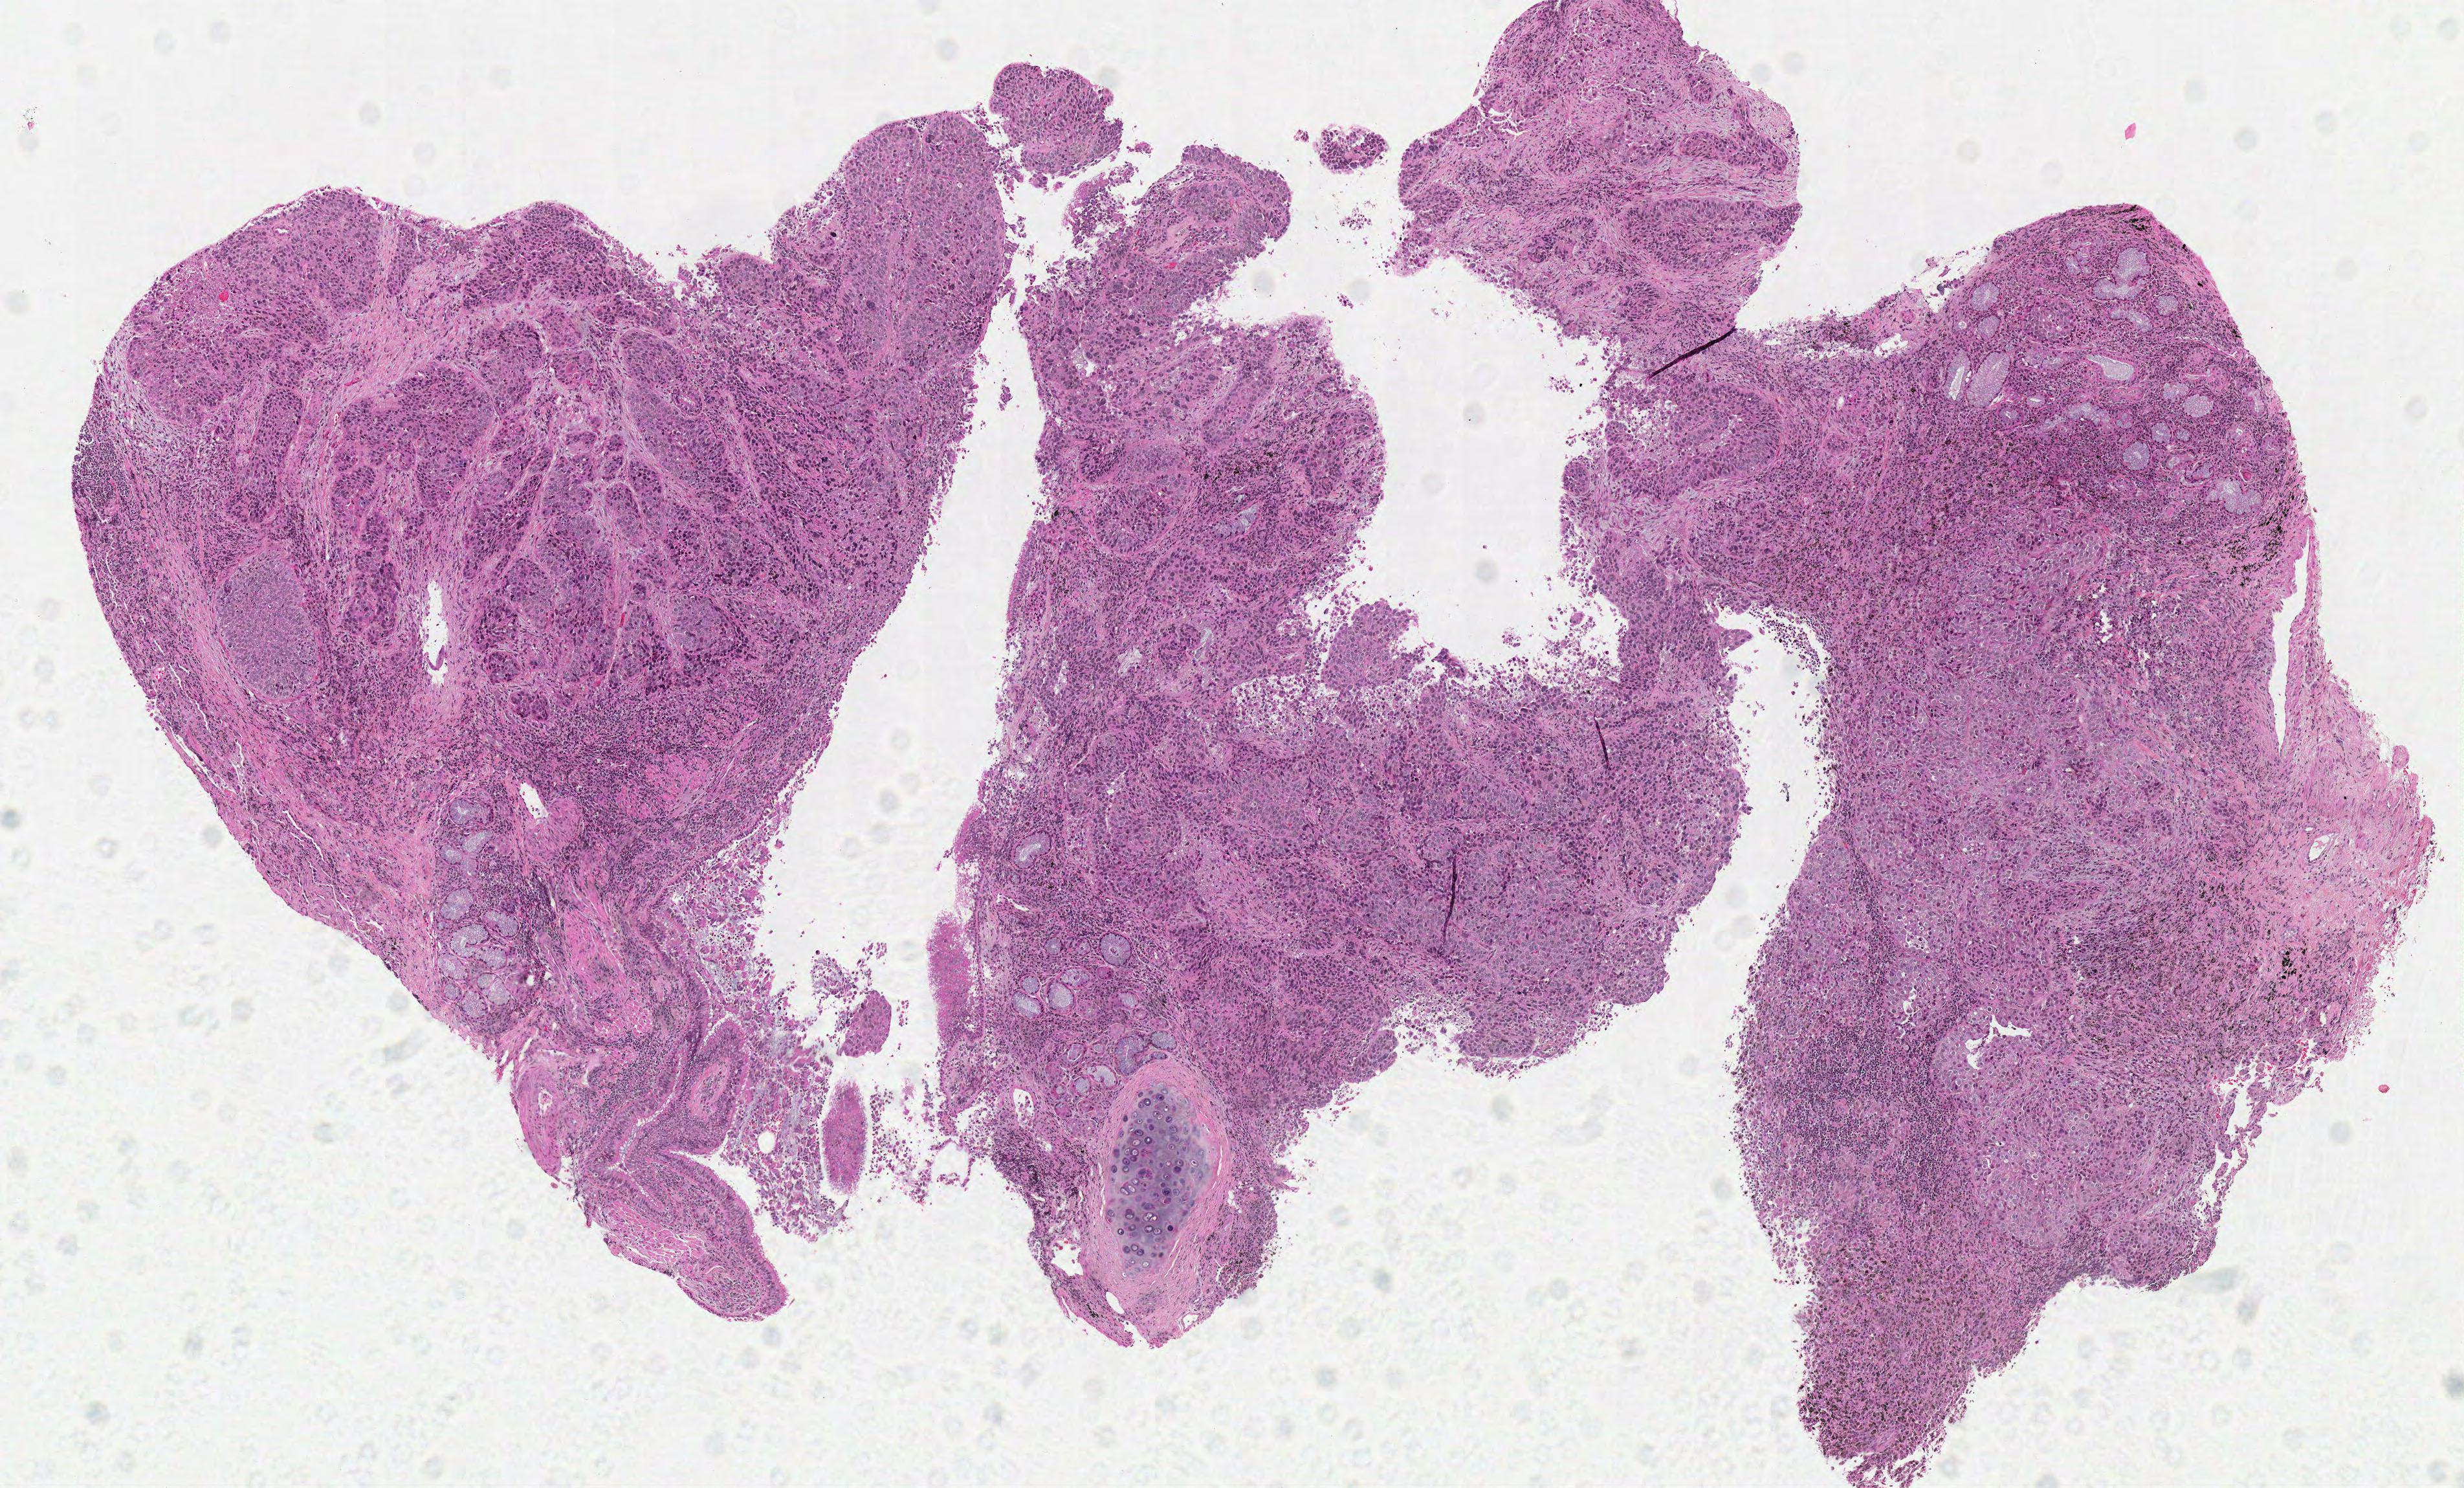
H&E-stained whole-slide image, a low-resolution overview of the entire scanned area, about 7.5 x 4.5 mm. Formalin-fixed paraffin-embedded (FFPE) diagnostic section. Primary tumour sample from the lung. Male patient; age at initial diagnosis 70 years.
Diagnosis: Squamous cell carcinoma, NOS (upper lobe, lung). TNM: T4 N0 M0. AJCC pathologic stage: IIIB.